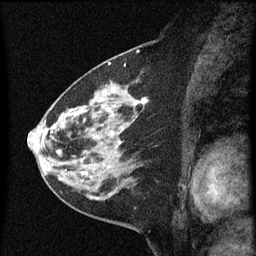
Breast MRI (dynamic contrast-enhanced), one sagittal slice. Dynamic contrast-enhanced series, image 2 of 3 at this slice position (ordered by acquisition). 1.5 T. TE 4.2 ms, TR 8 ms. 2 mm slice thickness. 256 × 256 image matrix. Patient: female, 60 years.
Annotated regions visible in this slice (semi-automatically segmented with operator editing):
- analysis volume of interest (the breast-tissue region the enhancement analysis was run in; not a lesion): box from (x=48, y=82) to (x=149, y=183) px
- tumour enhancement mask (voxels above the 70 % enhancement threshold inside the analysis volume of interest): (x=52, y=88)–(x=149, y=181)